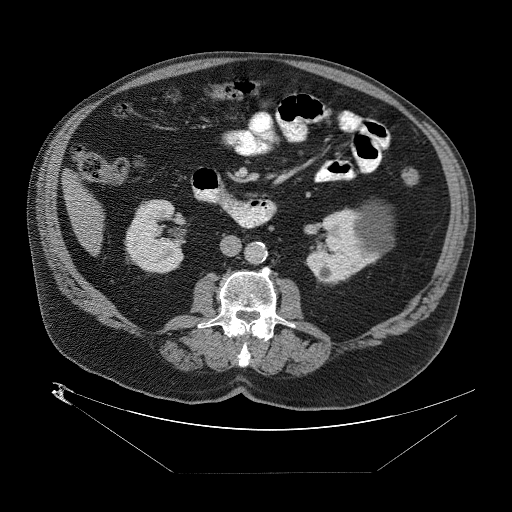
Contrast-enhanced abdominal CT (liver protocol), one axial slice; 140 kVp; one of 2 acquisitions stored at this slice position; soft-tissue window (W 400 / L 40 HU); 2.5 mm slice thickness; 512 × 512 image matrix, field of view 480 × 480 mm. Case-level facts recorded for this patient, not image findings: diagnosis: hepatocellular carcinoma (patient treated with transarterial chemoembolisation; whether this scan precedes or follows treatment is not stated here); TNM stage (as recorded): Stage-II; Child-Pugh class: B; tumour differentiation: moderately differentiated.
Outlined on this slice (semi-automatically segmented with operator editing):
- abdominal aorta: bounding box [x1, y1, x2, y2] px = [246, 242, 268, 265]
- liver parenchyma outside the tumour (the mass and vessels are separate outlines, so this box may not span the whole liver): [62, 166, 104, 250]